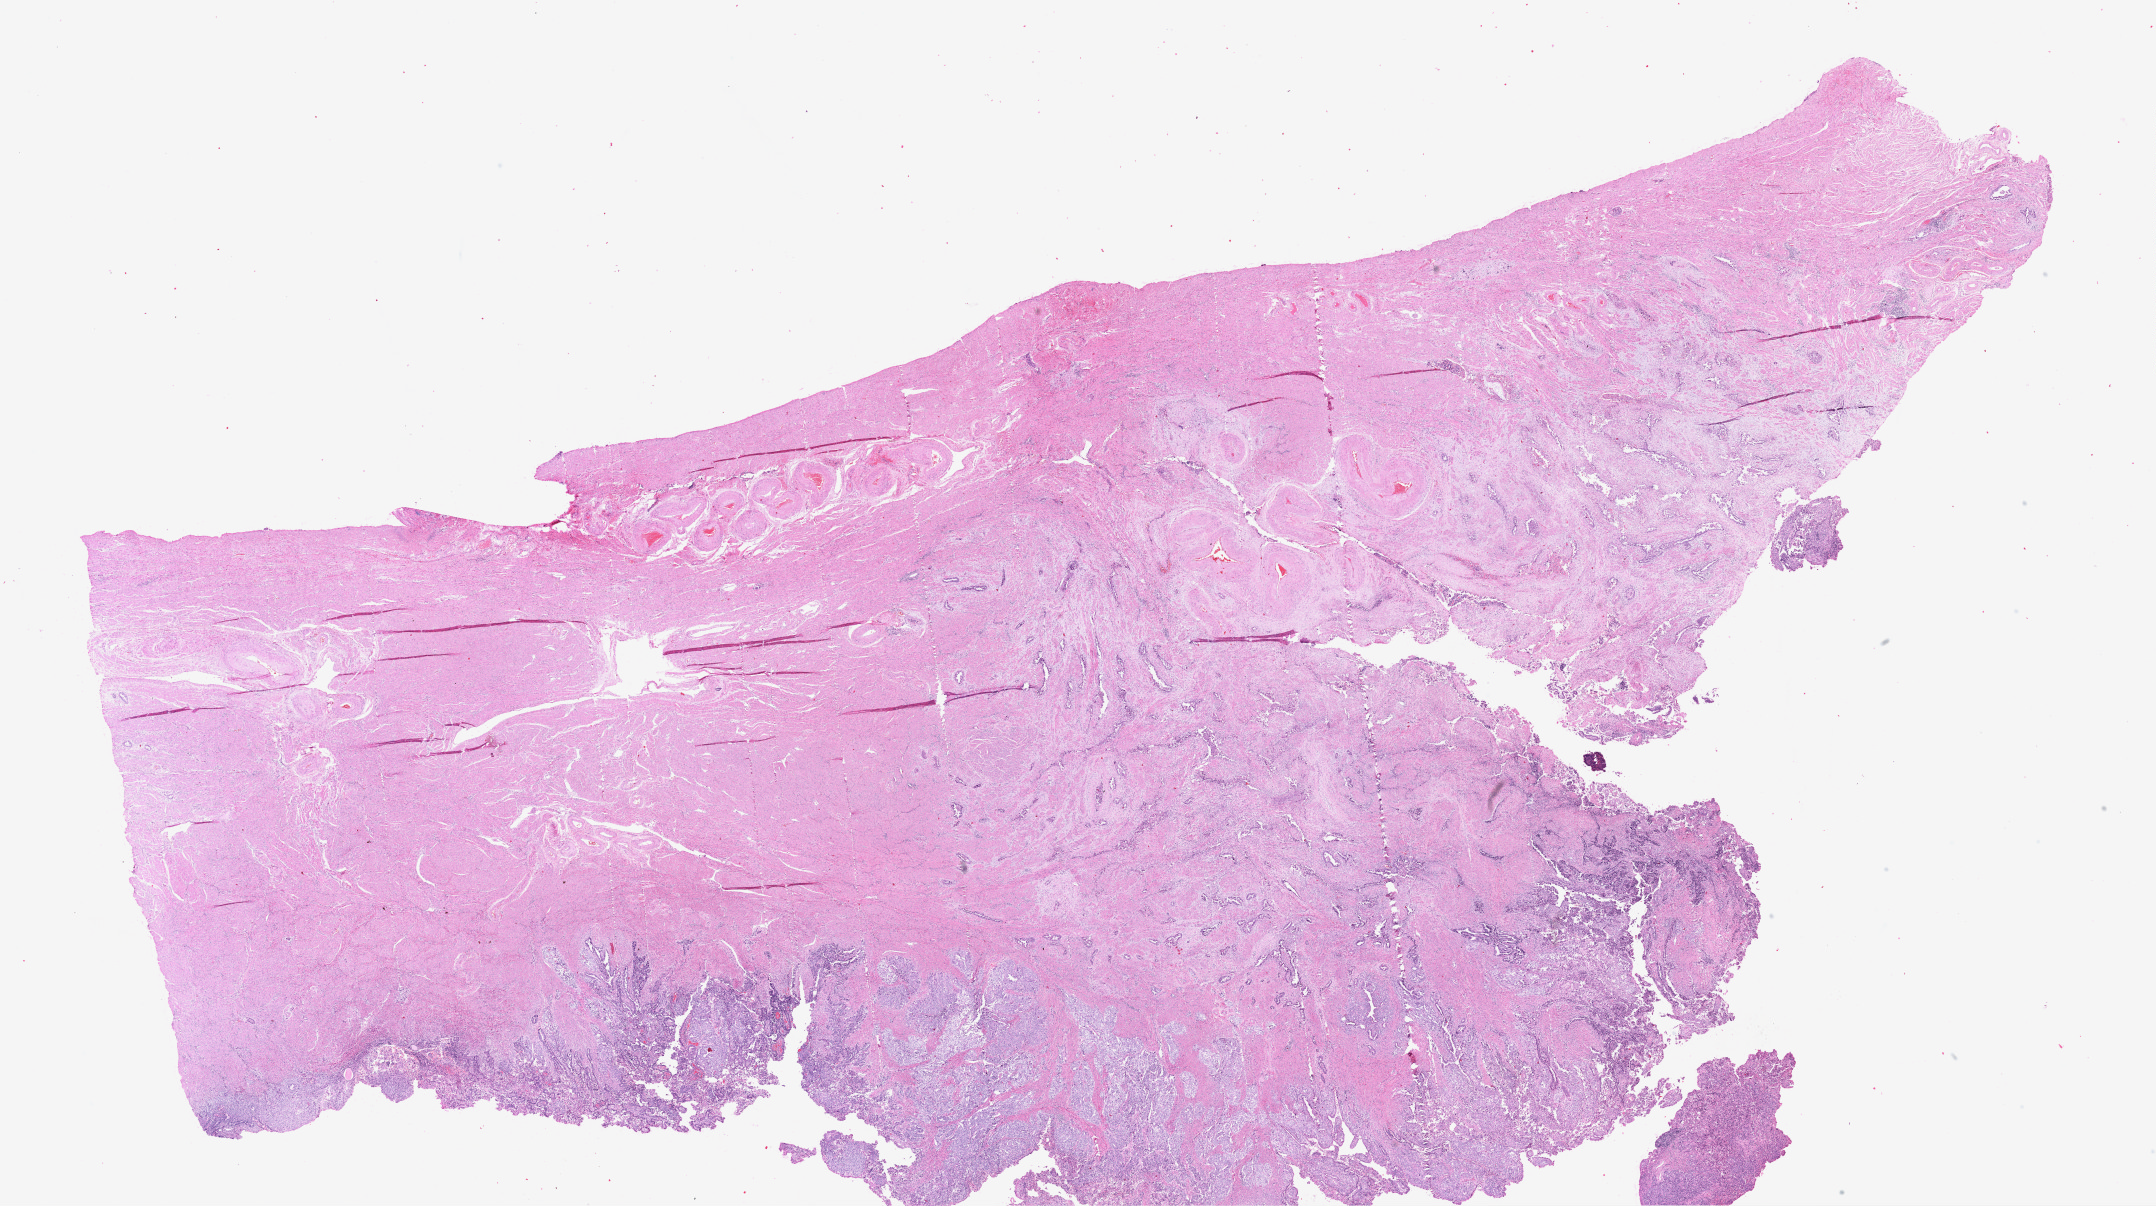
Digitized H&E tissue section (whole slide), a low-resolution overview of the entire scanned area, about 33.9 x 19.0 mm, formalin-fixed paraffin-embedded (FFPE) diagnostic section, sample: primary tumour, uterus. Patient: female, age at initial diagnosis 62 years. Histologic grade: G3 (poorly differentiated).
FIGO stage: IIIC2. Pathologic diagnosis: Serous cystadenocarcinoma, NOS (endometrium).